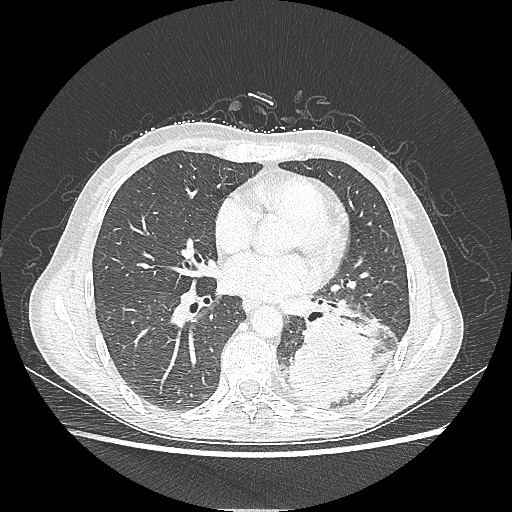
Chest CT, one axial slice; position 103 of 220 along the scan axis; lung window (W 1500 / L -600 HU); 512 × 512 image matrix, field of view 360 × 360 mm. Patient: female, 53 years. From the clinical record (not read from this slice): clinical TNM (as recorded): T3 N0 M0.
Outlined on this slice (bounding box drawn by a radiologist):
- lung tumour (recorded histology: adenocarcinoma): bounding box [x1, y1, x2, y2] px = [287, 307, 401, 409]